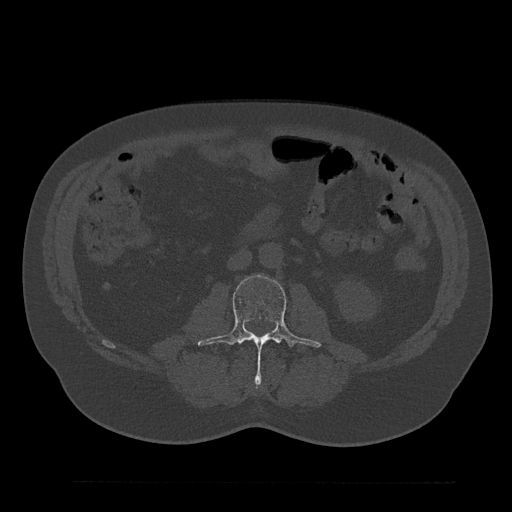
CT including the spine, one axial slice; reconstruction kernel Br40s/3; 120 kVp; bone window (W 1800 / L 400 HU); 0.5 mm slice thickness; 512 × 512 image matrix. Patient: male, 61 years. Case-level facts recorded for this patient, not image findings: primary cancer: prostate.
Structures marked on this image (semi-automatic segmentation, software-assisted and operator-edited):
- L3 vertebra: box from (x=198, y=275) to (x=322, y=383) px